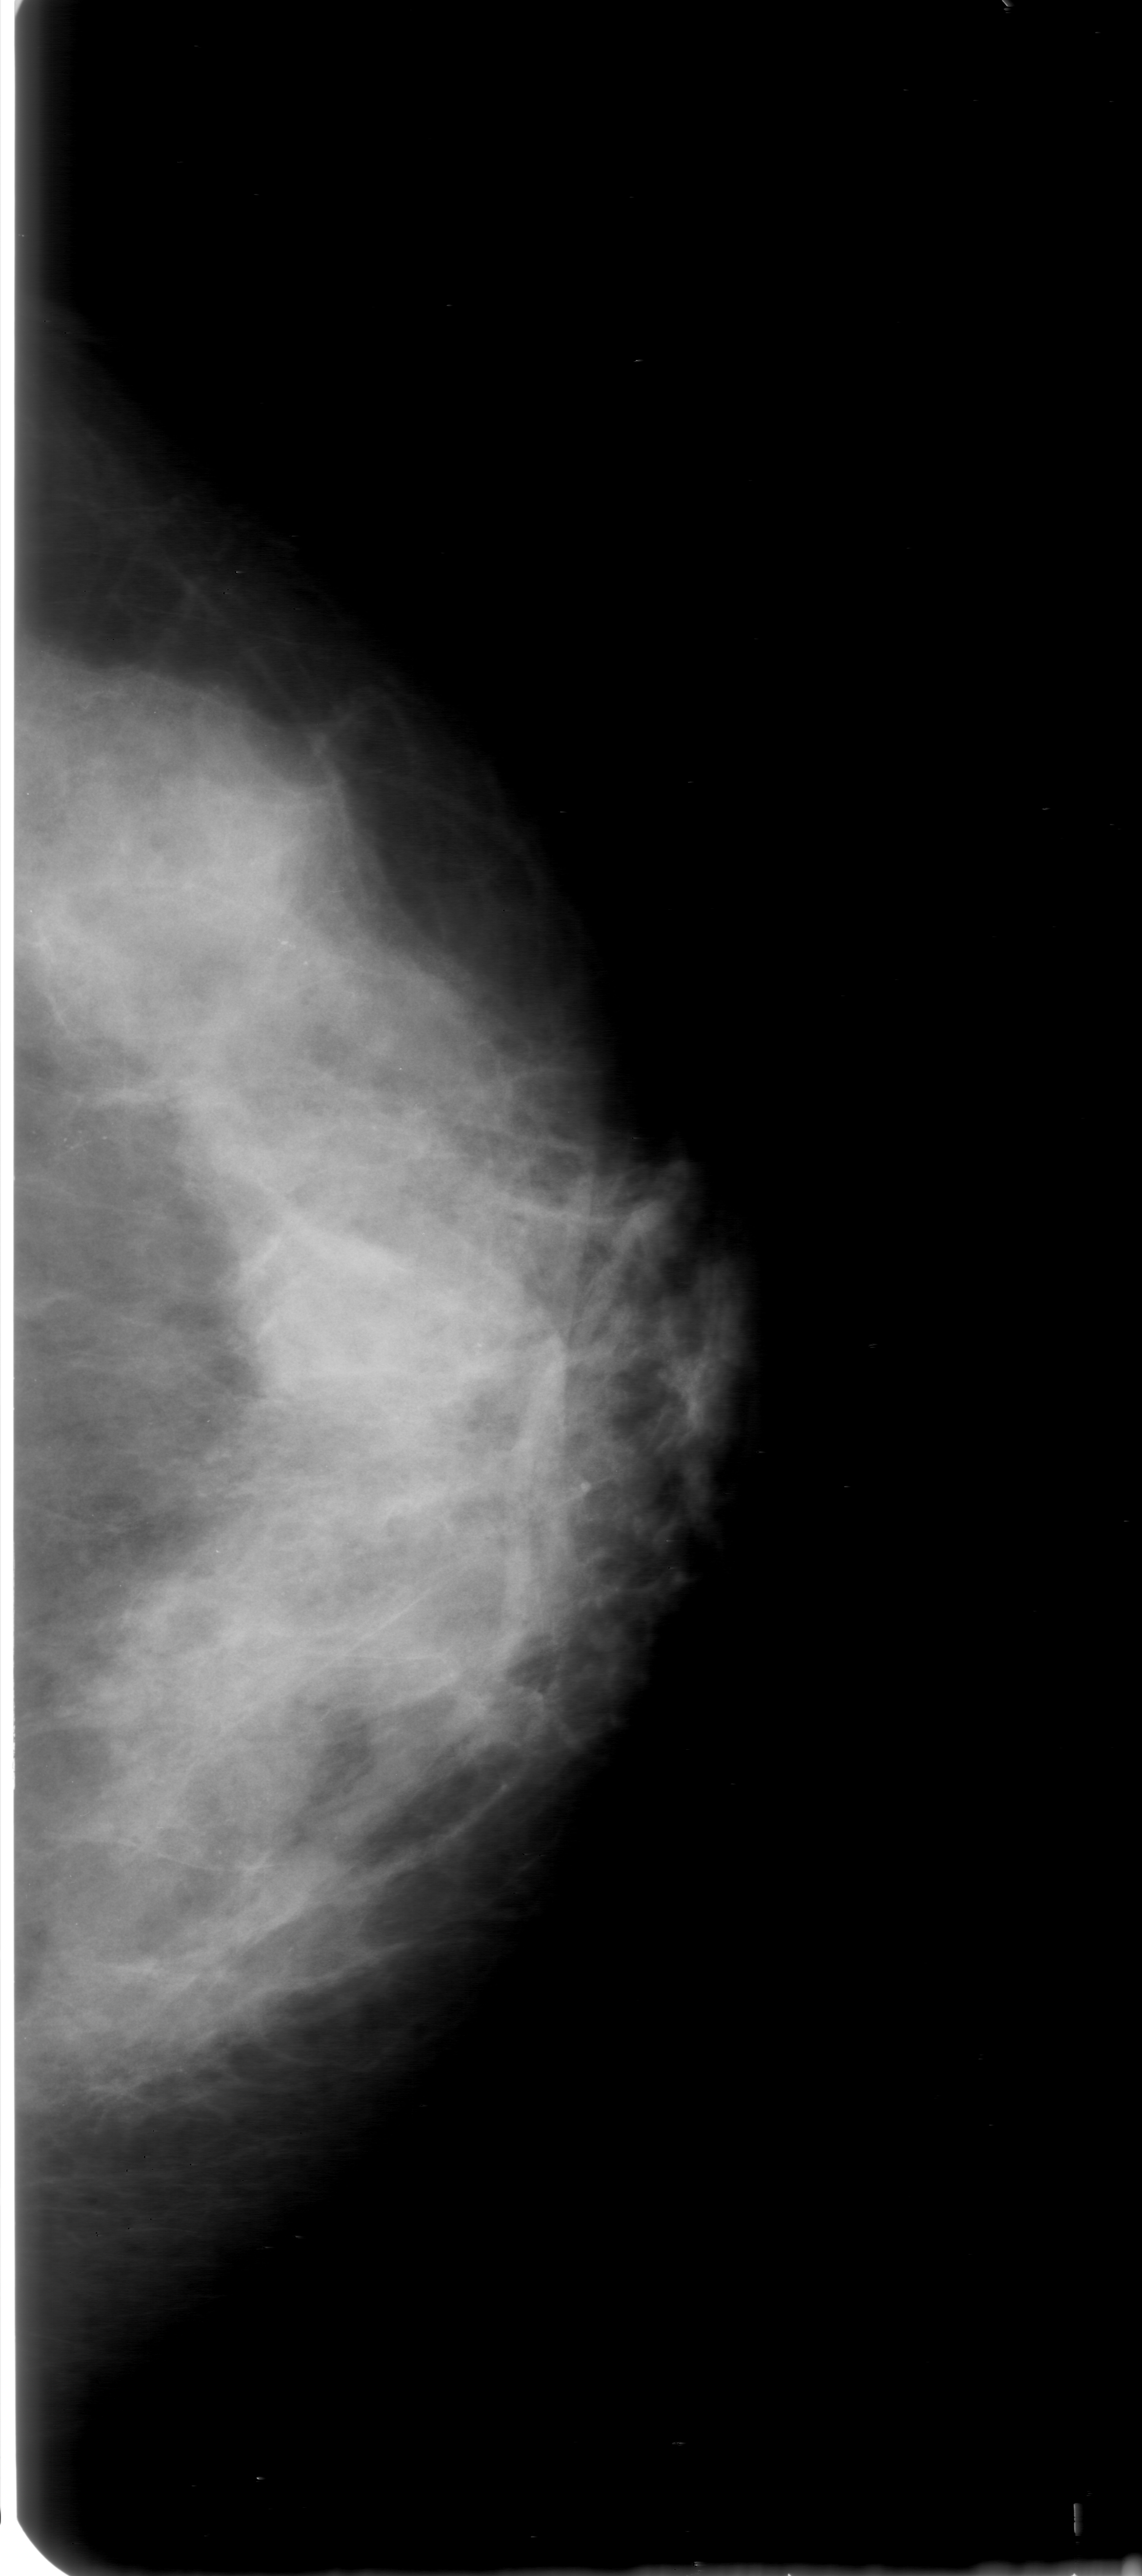
Scanned film-screen mammogram. Left breast. CC view. Breast composition: extremely dense (BI-RADS density category 4 of 4). 1142 × 2576 image matrix.
Marked abnormalities (boxes around the expert regions of interest):
- calcifications, morphology pleomorphic, distribution clustered; BI-RADS assessment category 0 (incomplete: needs additional imaging); subtlety rating 3 on a 1 (subtle) to 5 (obvious) scale; pathology (as recorded): malignant: bounding box [x1, y1, x2, y2] px = [12, 1054, 144, 1203]